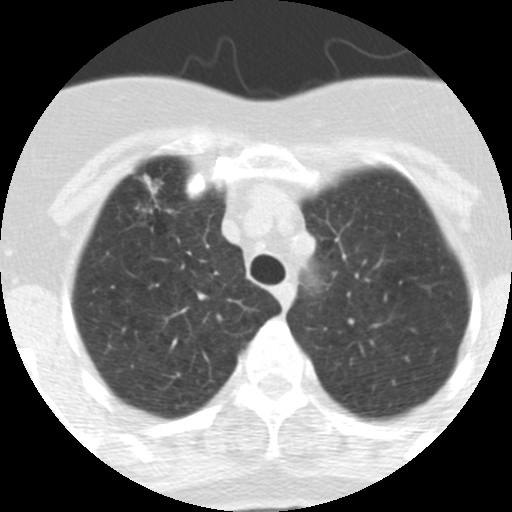
Chest CT (low-dose screening protocol), one axial image, baseline screening round, lung window (W 1500 / L -600 HU), standard (soft-tissue) reconstruction kernel (STANDARD), 512 × 512 image matrix. Female participant, aged 62 years at enrolment. Current smoker at enrolment.
• Lesion marked by an expert reader, bounding box (x1, y1, x2, y2) in pixels: (116, 170, 189, 237).
• Screening reader's record for this exam (one nodule recorded; not confirmed to be the boxed lesion): non-calcified nodule or mass ≥4 mm, right upper lobe, 9 × 7 mm, spiculated (stellate) margins, soft tissue attenuation.
• Lung cancer was diagnosed 126 days after this screen: adenocarcinoma, NOS, right upper lobe, moderately differentiated (G2), stage IA (AJCC 6th edition), 18 mm at pathology.